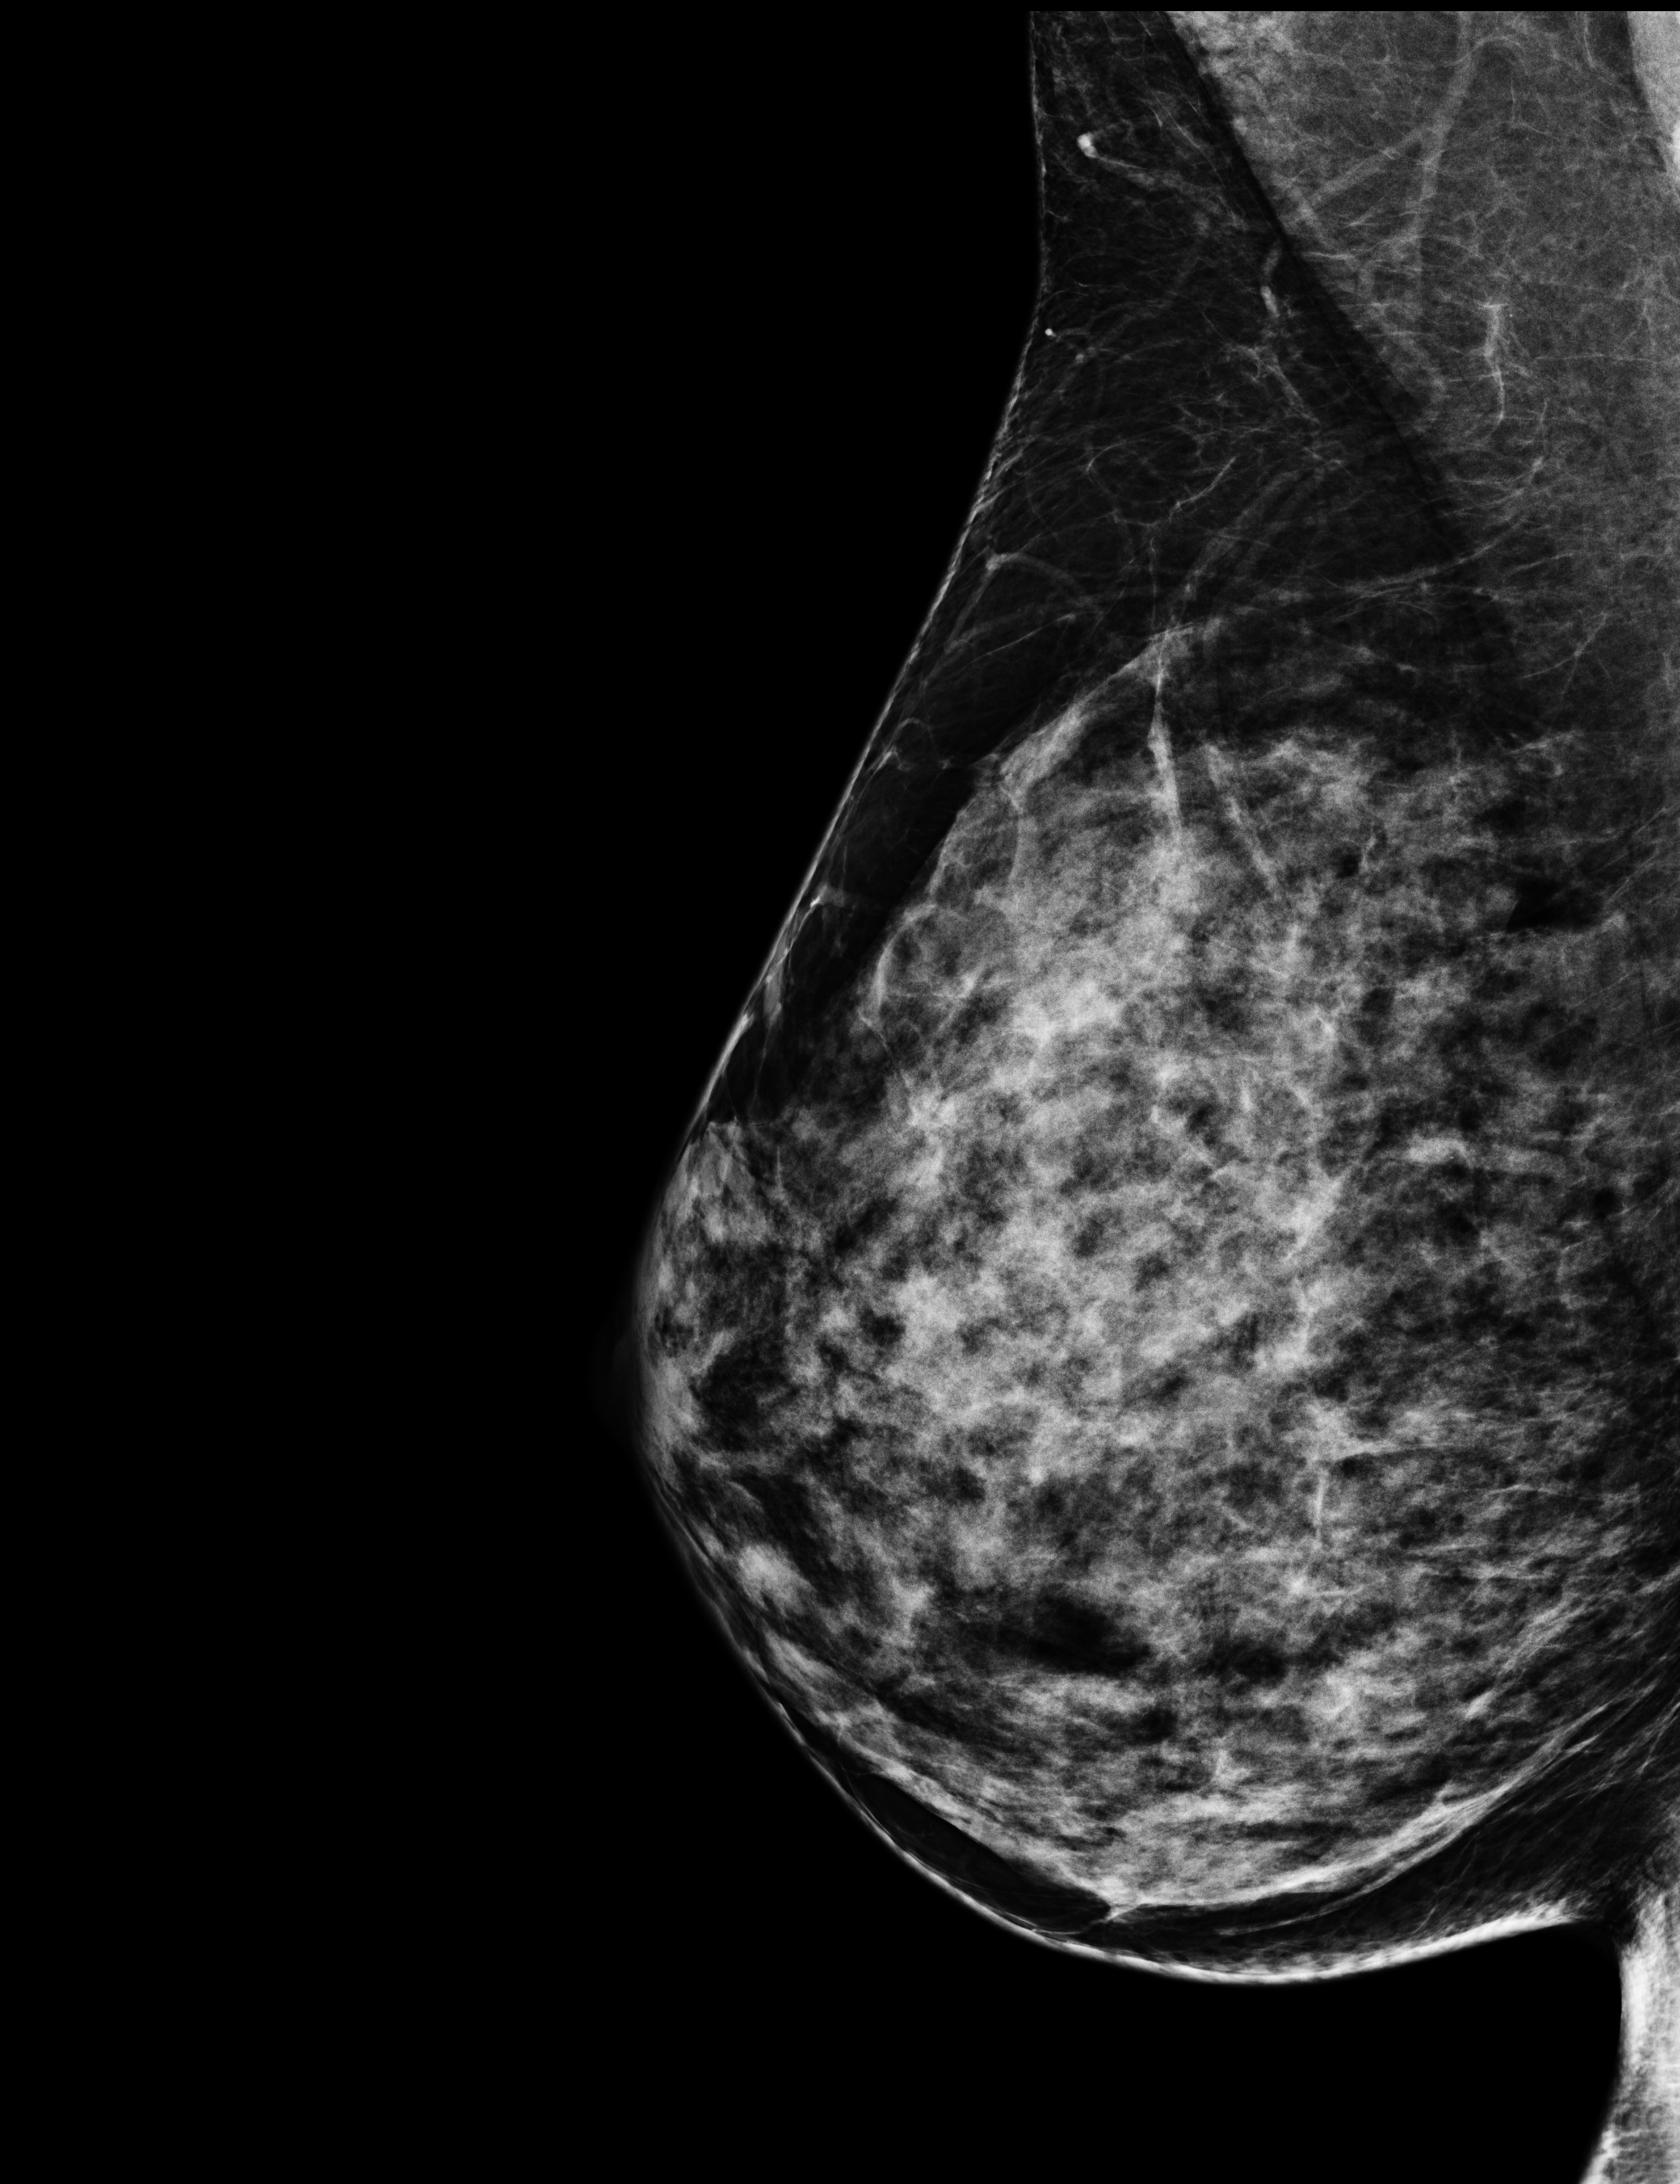
Digital mammogram (FFDM); right breast; medio-lateral oblique projection; screening examination; compressed breast thickness 51 mm. Female patient, age 42 years.
Breast density at the screening exam (both breasts): extremely dense (BI-RADS density category d). Final BI-RADS assessment for this screening round (tomosynthesis exam, both breasts): category 1. Recall: no recall after this screen.